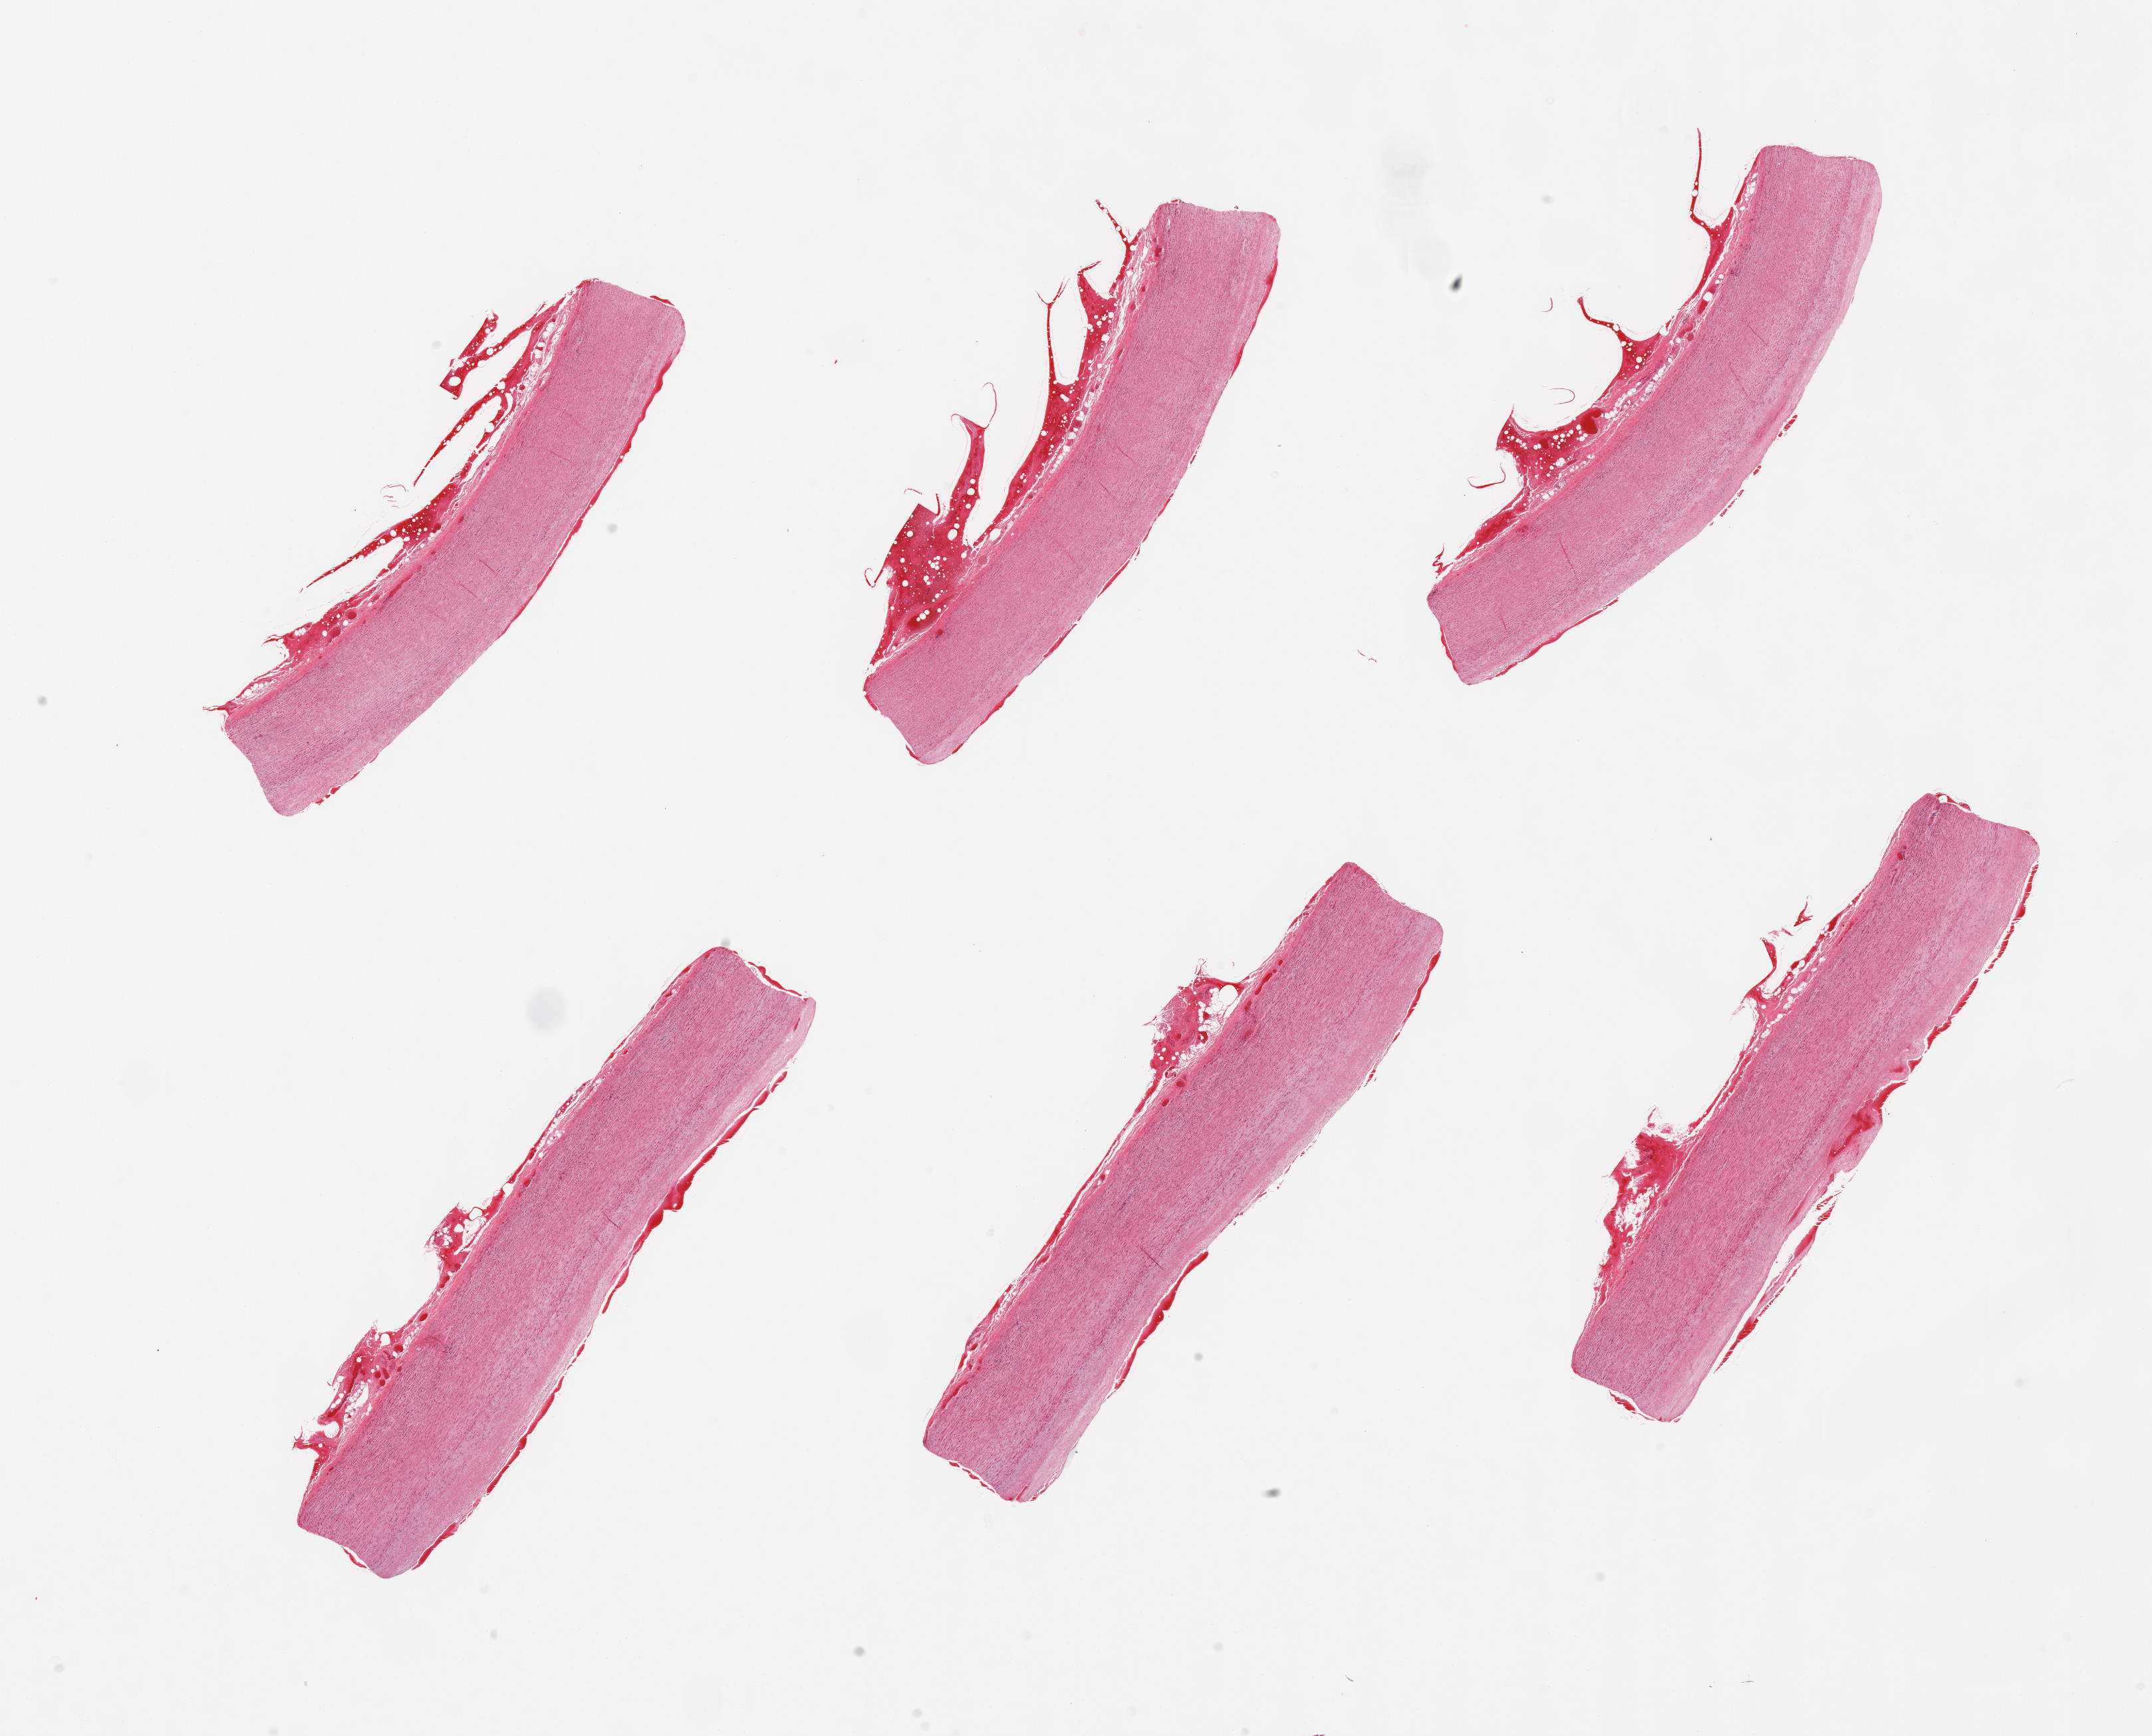
Whole-slide image, hematoxylin and eosin (H&E) stain, low-resolution overview of the scanned area, about 25.6 x 20.6 mm, PAXgene-fixed, paraffin-embedded tissue, section of aorta (target tissue), donor tissue sample. Donor: male.
Pathologist's review note for this sample: 6 pieces; no plaque; periaortic hemorrhage.